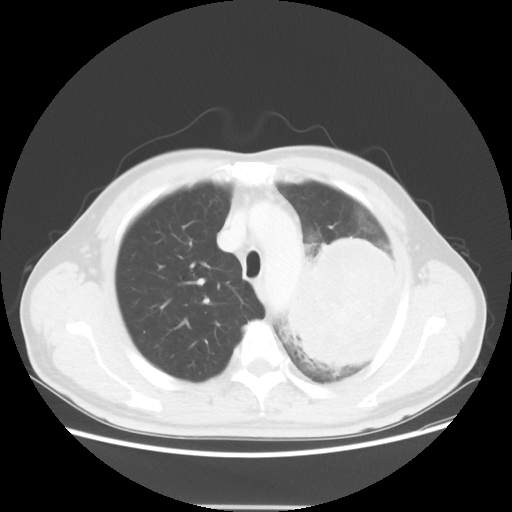
Chest CT, one axial slice. Position 42 of 53 along the scan axis. Reconstruction kernel STANDARD. 100 kVp. Lung window (W 1500 / L -600 HU). 5 mm slice thickness. 512 × 512 image matrix, field of view 391 × 391 mm. Male patient, age 60 years. Case-level facts recorded for this patient, not image findings: clinical TNM (as recorded): T4 N1 M1a; histopathological grade: G3.
Outlined on this slice (rectangle marked by the reading radiologist):
- lung tumour (recorded histology: large cell carcinoma): bounding box <278,228,407,374> (left, top, right, bottom; pixels)